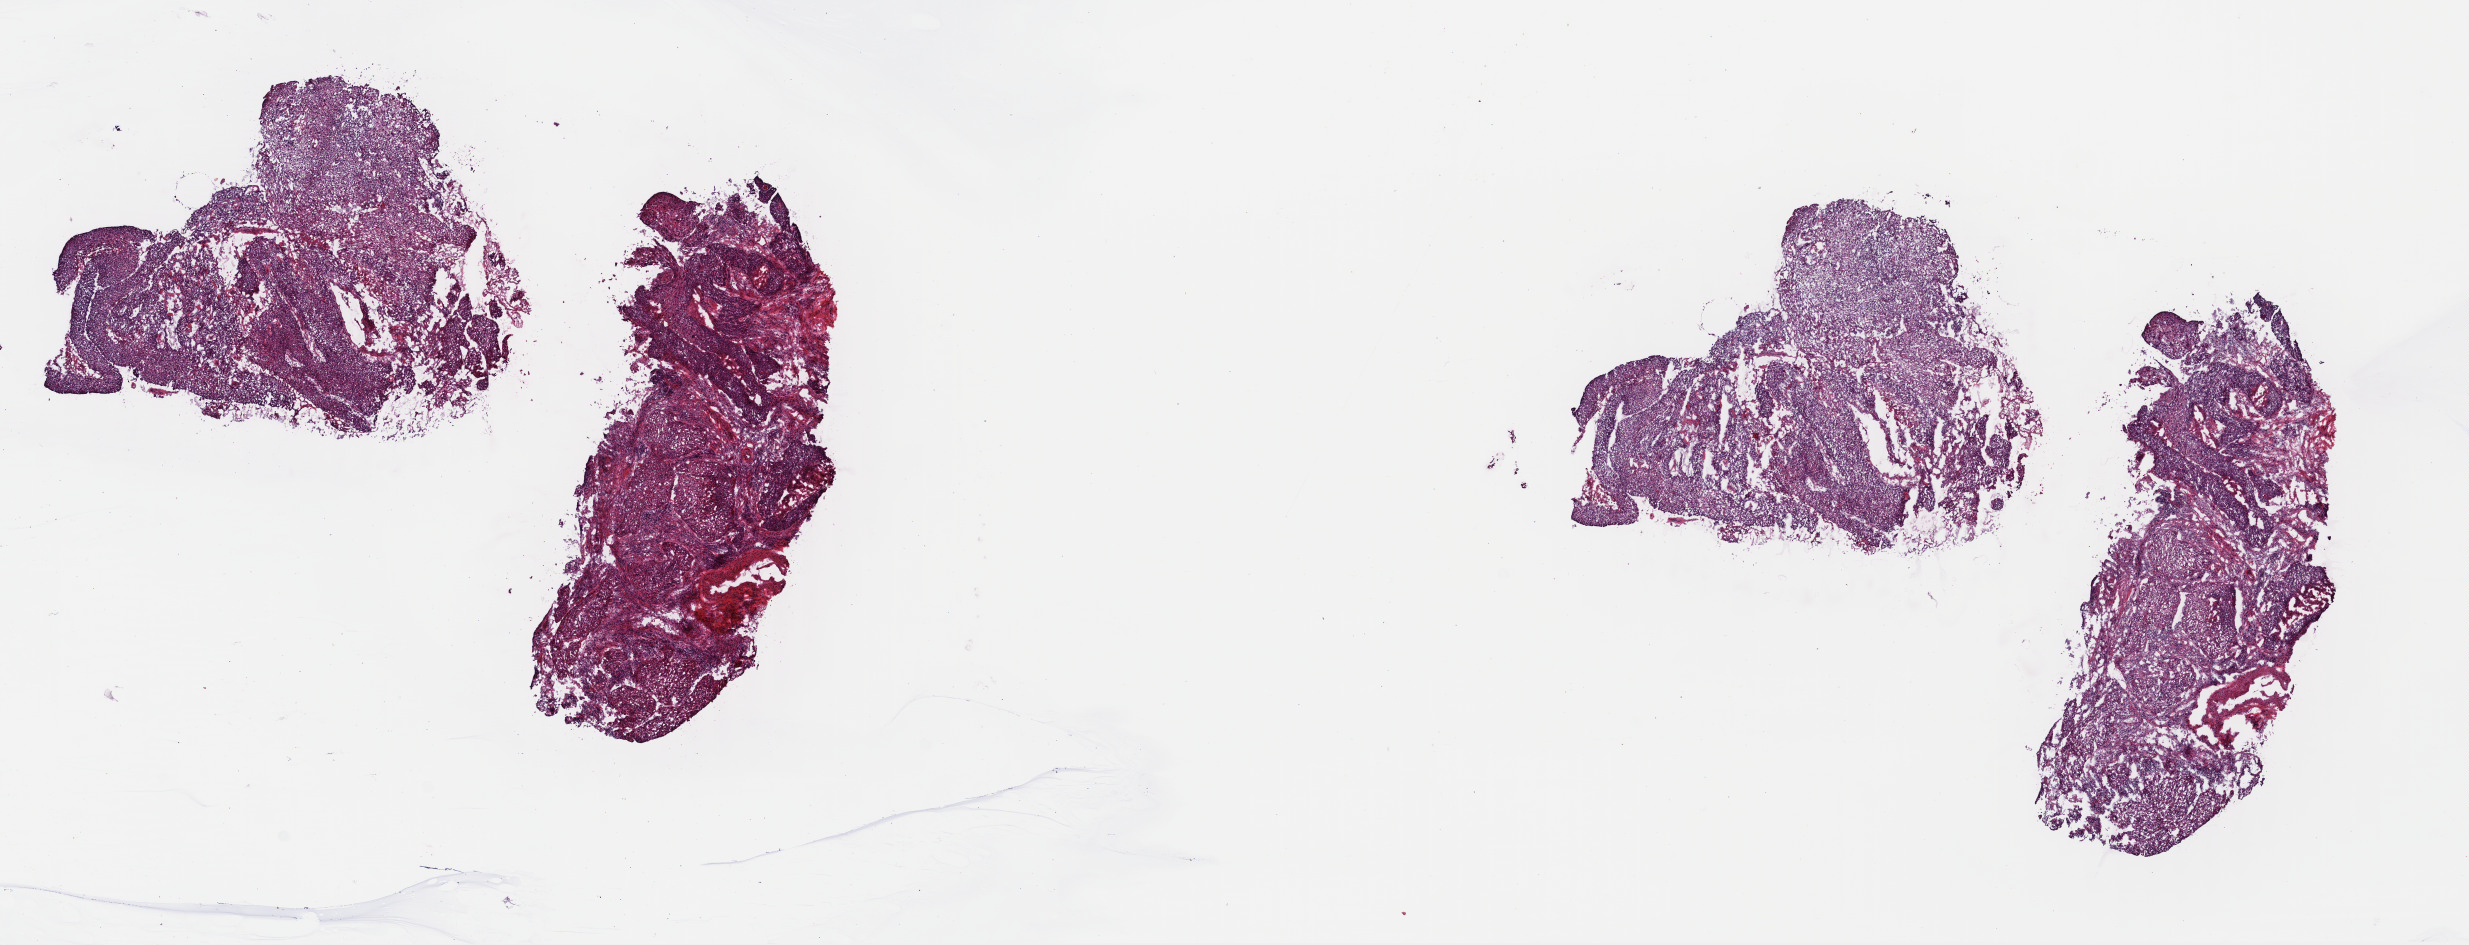
Whole-slide histology image, H&E-stained — whole scanned area (about 19.4 x 7.4 mm) shown as a low-resolution overview. Frozen section from the top of the tissue portion. Cervix, primary tumour sample. Female patient; age at initial diagnosis 64 years. Histologic grade: G3 (poorly differentiated). Pathologist review of this section (percent, as recorded): tumour cells 100%, tumour nuclei 80%, normal cells 0%, stromal cells 0%, necrosis 0%. Infiltration values recorded for this section: lymphocyte infiltration 3%, monocyte infiltration 0%, neutrophil infiltration 0%.
Pathologic diagnosis: Squamous cell carcinoma, NOS.